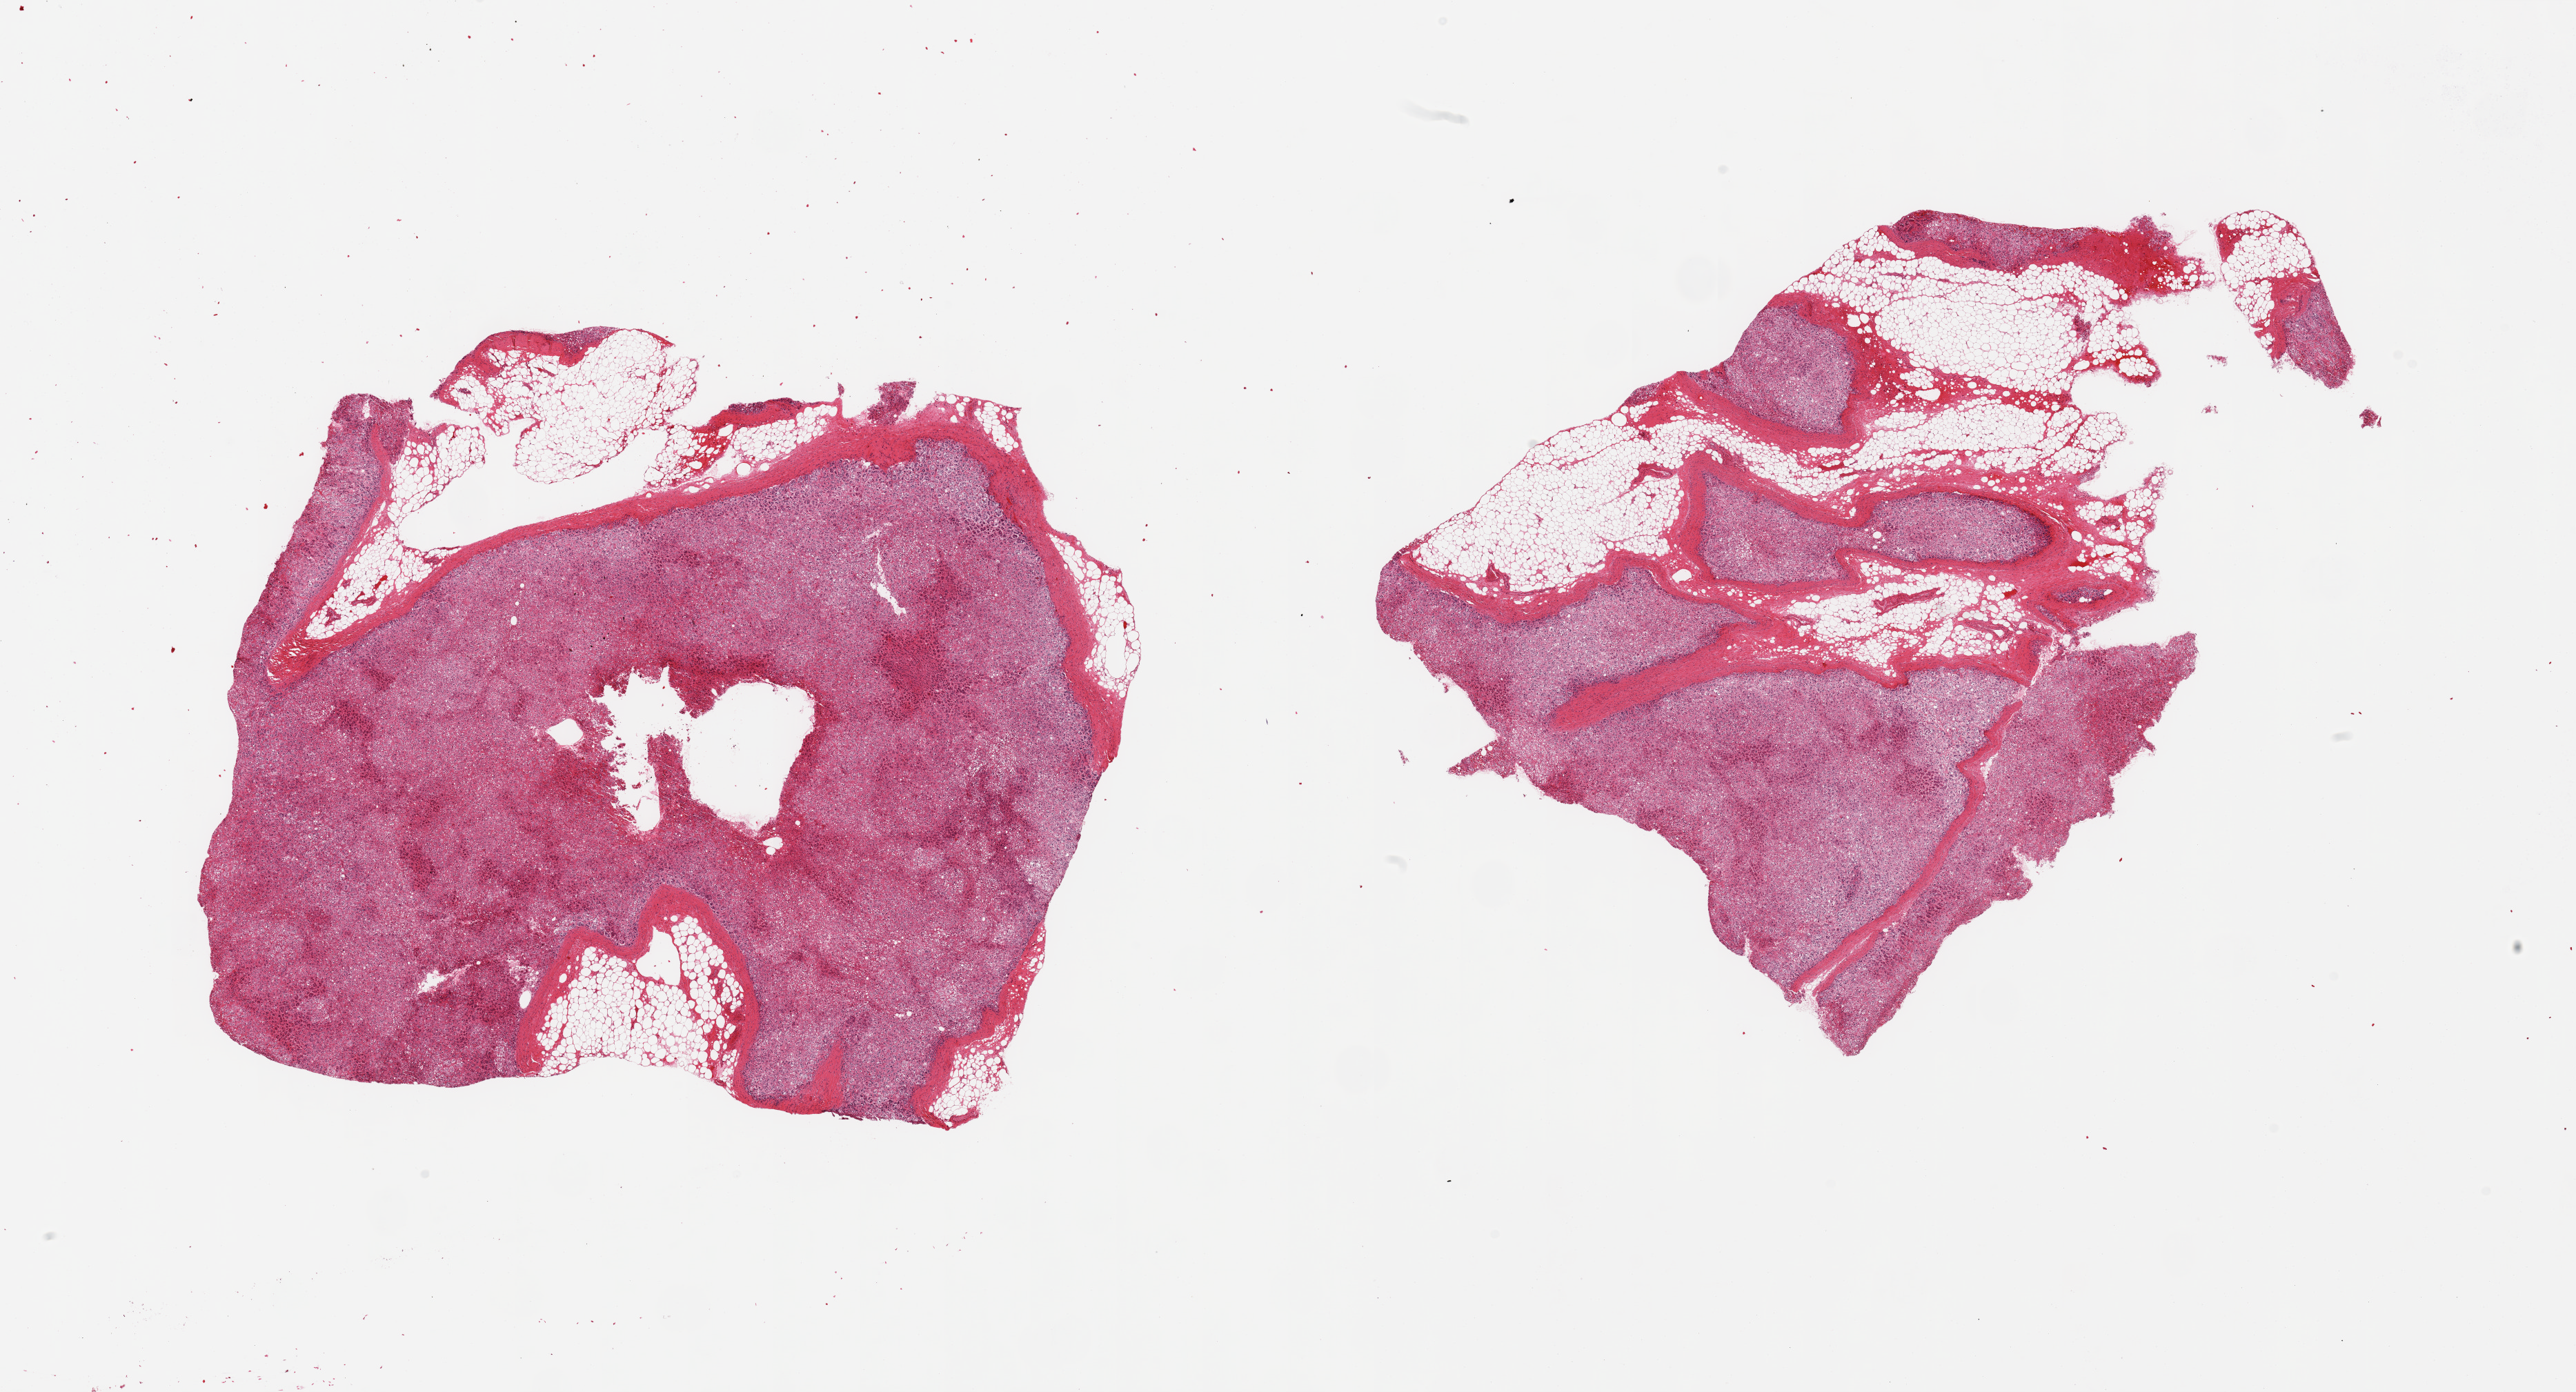
H&E whole-slide image, brightfield, a low-resolution overview of the entire scanned area, about 29.5 x 16.0 mm (acquisition: 20x scan). PAXgene-fixed paraffin-embedded (PFPE) section. Sampled site (target tissue): adrenal gland. Donor tissue sample. Donor sex: male.
Reviewer comment on this tissue sample: 2 pieces; 30 and 40% internal and external fat.